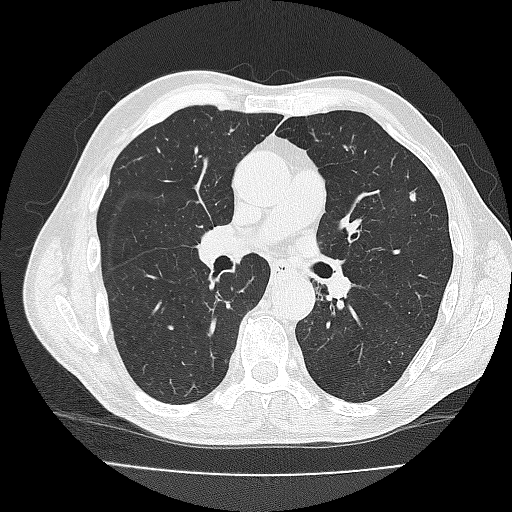
Axial slice from a low-dose chest CT screening exam, second screening round (one year after baseline), lung window (W 1500 / L -600 HU), 2 mm slice thickness, reconstruction kernel FC30 (as recorded), slice 96 of 206 in the series, 512 × 512 image matrix, field of view 359 × 359 mm. Male, age 71 years at enrolment. Current smoker at enrolment.
- Expert reader's lesion annotation, bounding box <389,179,430,221> (left, top, right, bottom; pixels).
- Screening reader's record for this exam: no non-calcified nodule ≥4 mm recorded.